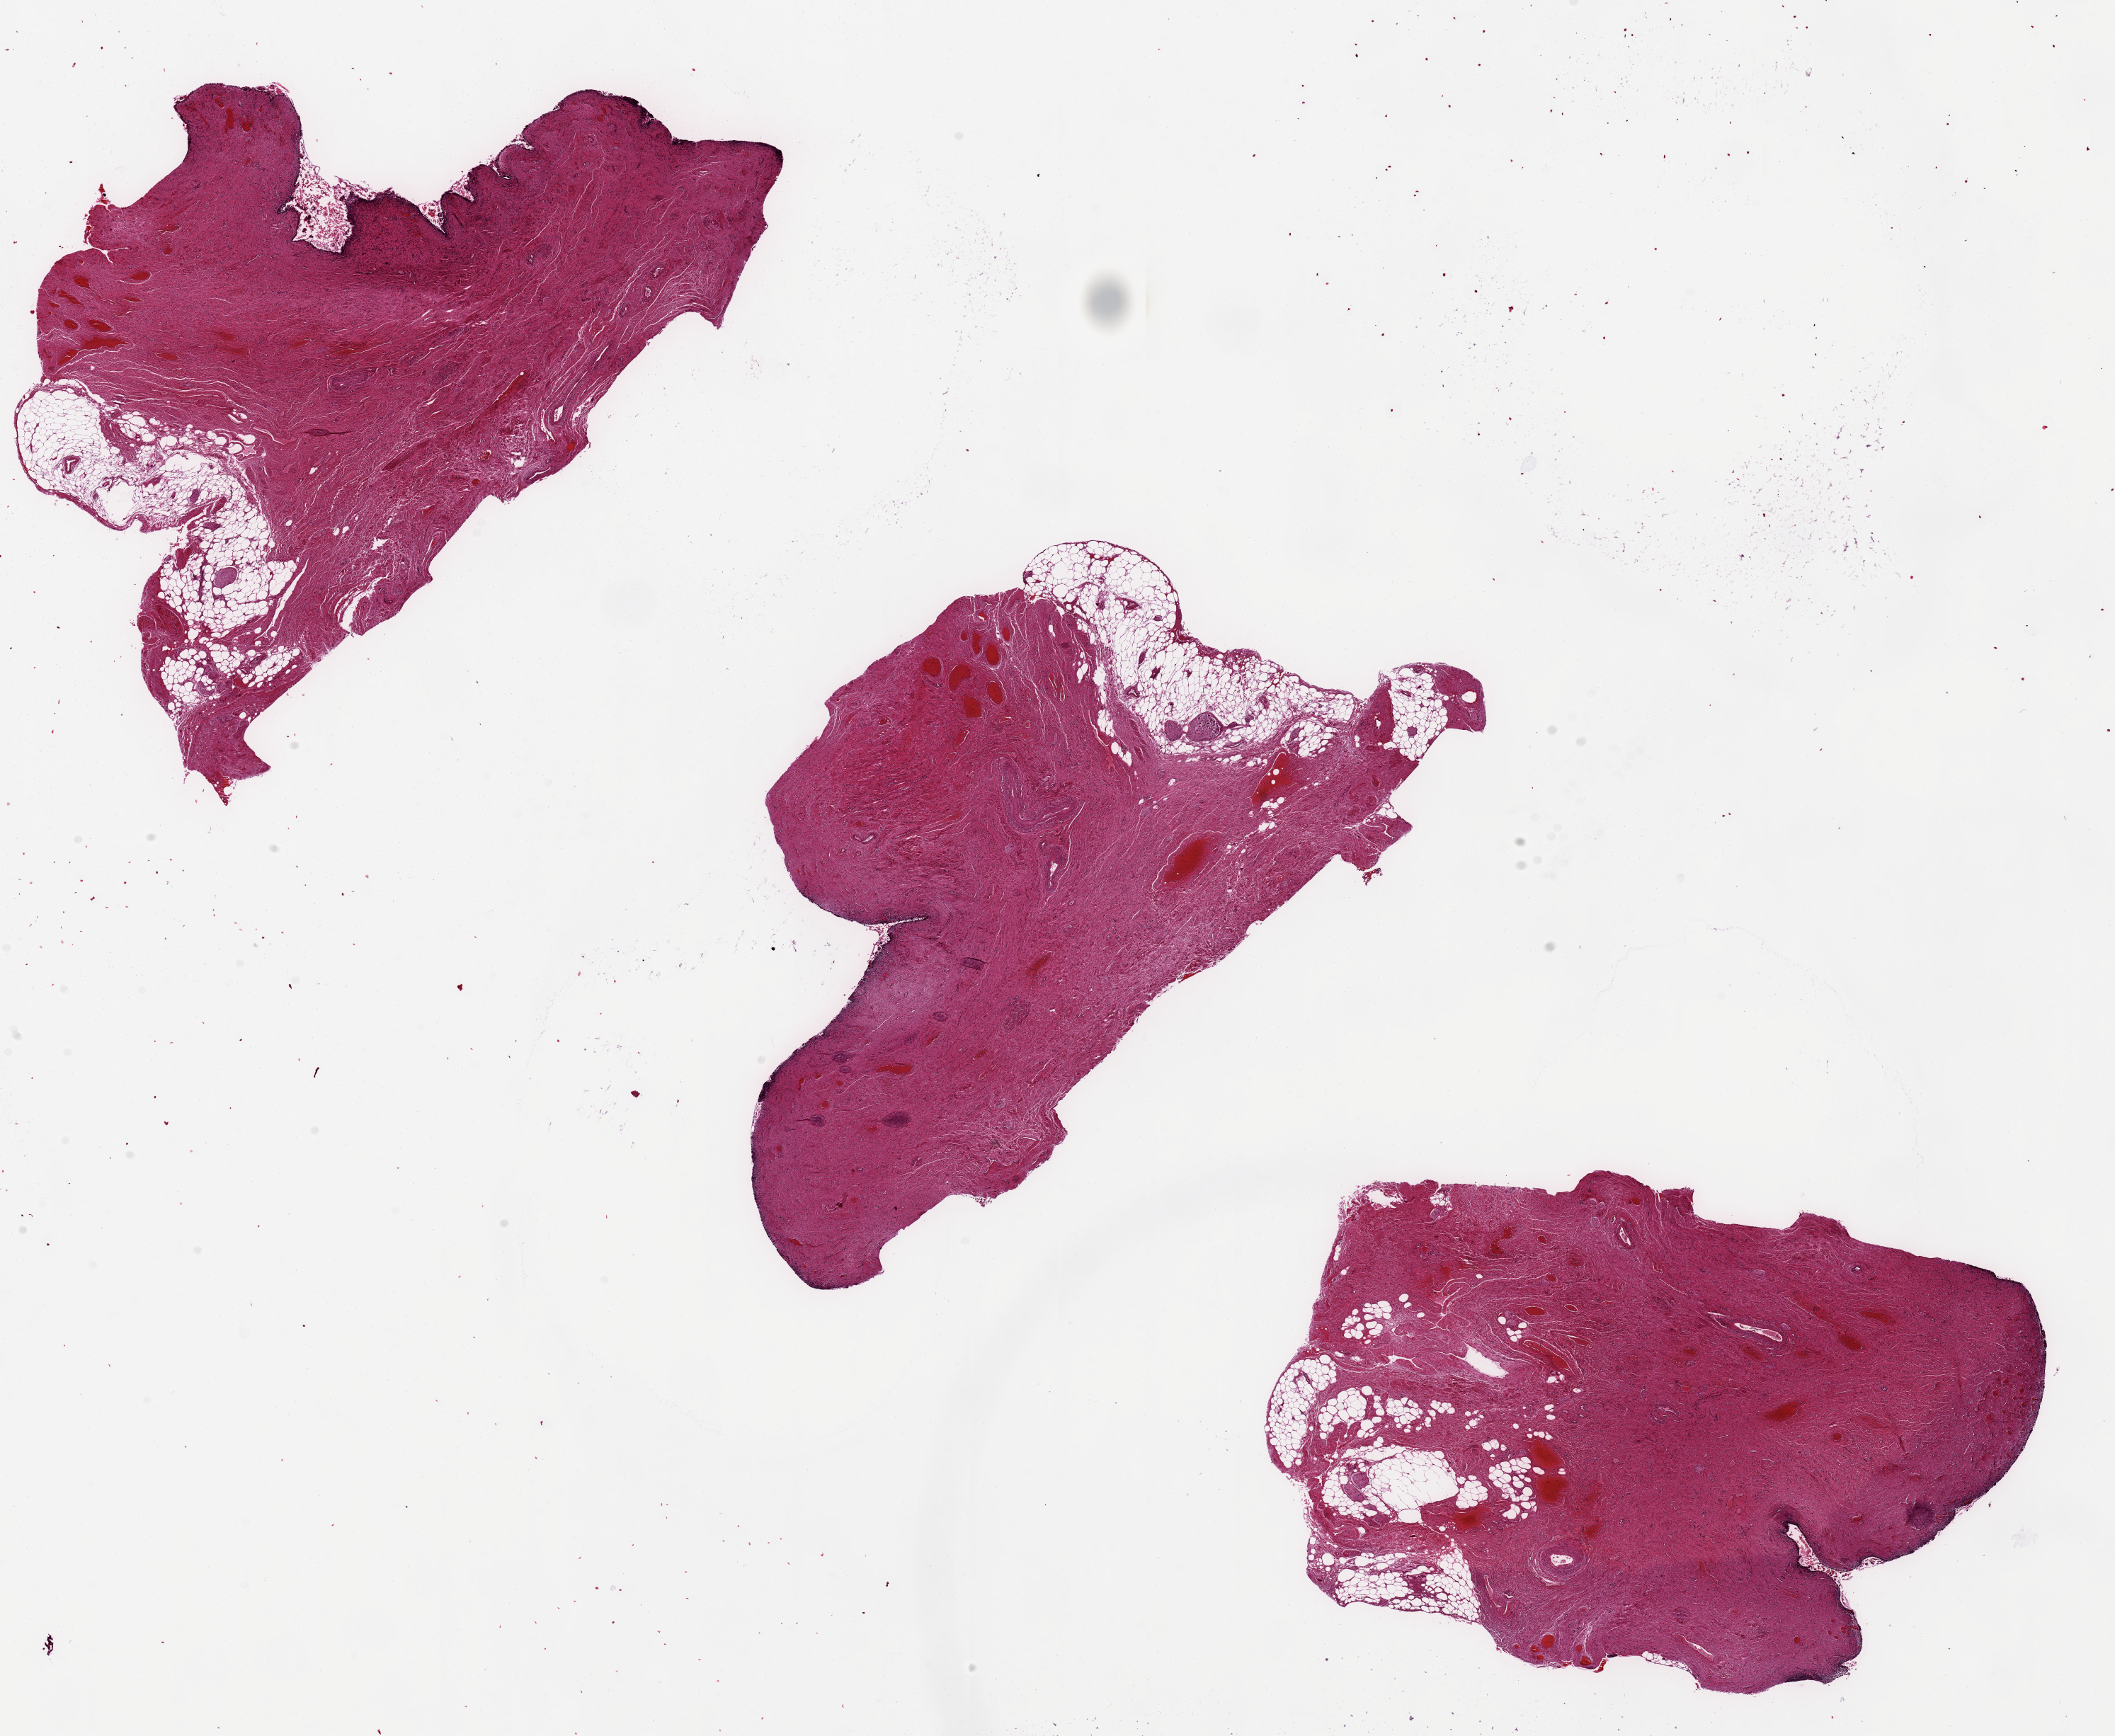
Digitized hematoxylin and eosin (H&E)-stained section, a low-resolution overview of the entire scanned area, about 23.6 x 19.4 mm (acquisition: 20x scan). PAXgene-fixed paraffin-embedded (PFPE) section. Sampled site (target tissue): vagina. Donor tissue sample. Female donor.
Reviewer comment on this tissue sample: Mucosa, 1 stroma. Moderate chr.